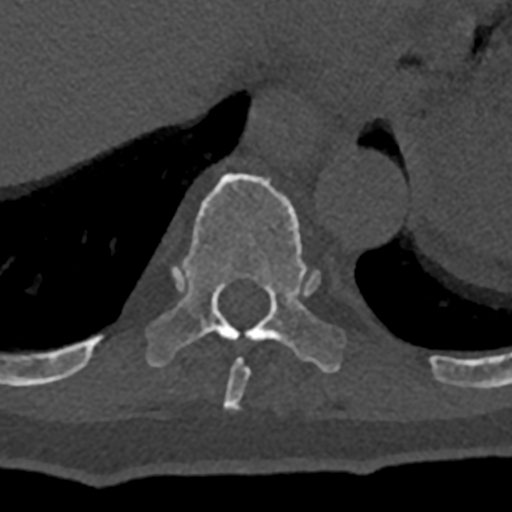
CT including the spine, one axial slice. Slice 611 of 797 in the series (ordered by position). Reconstruction kernel Br40s/3. Bone window (W 1800 / L 400 HU). 512 × 512 image matrix, field of view 160 × 160 mm. Patient: male, 74 years. Case-level facts recorded for this patient, not image findings: primary cancer: renal; vertebrae with lytic lesions (as recorded): T10, L1, L2, L3, L4, L5.
Structures marked on this image (semi-automatic segmentation, software-assisted and operator-edited):
- T10 vertebra: bounding box [x1, y1, x2, y2] px = [70, 173, 345, 375]
- T9 vertebra: [223, 358, 250, 412]